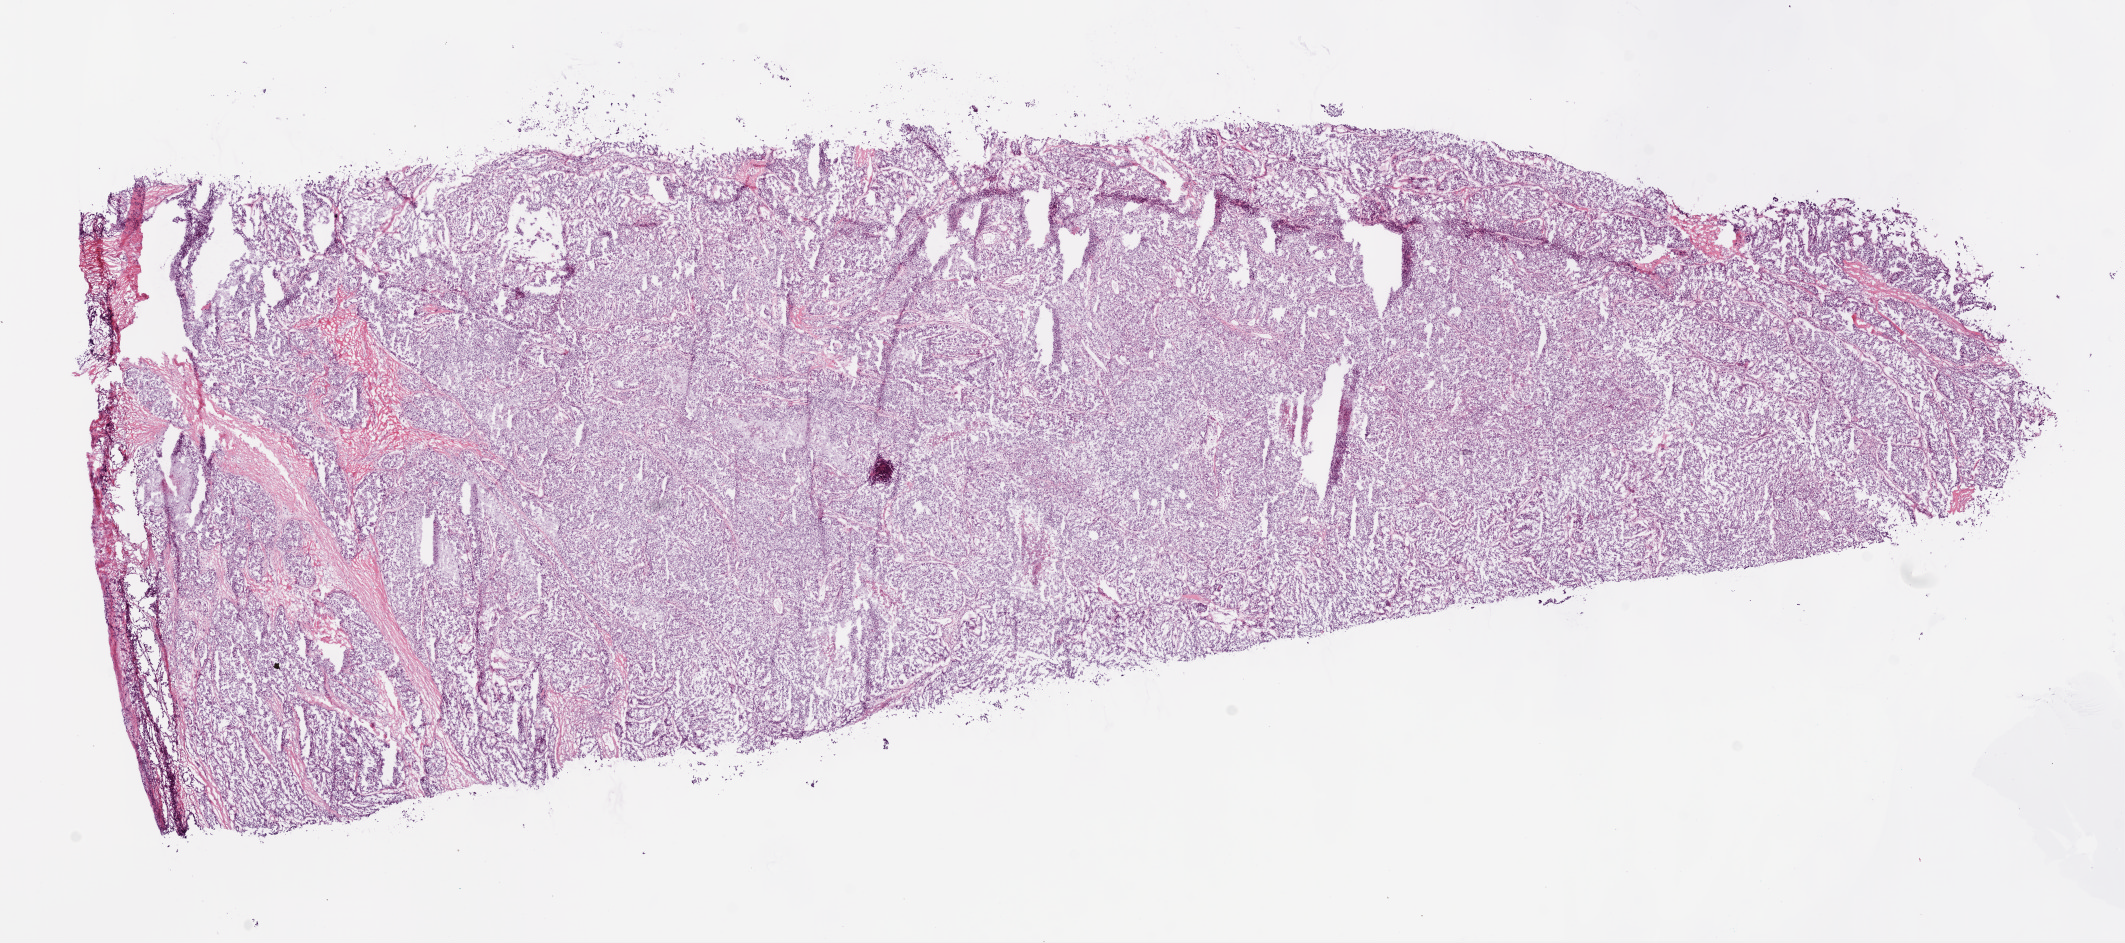
Whole-slide histology image, Hematoxylin and eosin (H&E) stained, a low-resolution overview of the entire scanned area, about 17.1 x 7.6 mm (slide scanned at 20x); frozen section from the bottom of the tissue portion; sample: primary tumour, kidney. Patient: male, age at initial diagnosis 33 years. Histologic grade: G3 (poorly differentiated). Pathologist review of this section (percent, as recorded): tumour cells 90%, tumour nuclei 85%, normal cells 0%, stromal cells 10%, necrosis 0%.
* lymph nodes positive (case pathology): 1 of 1 examined
* pathologic diagnosis: Clear cell adenocarcinoma, NOS
* laterality: right
* AJCC pathologic stage: IV